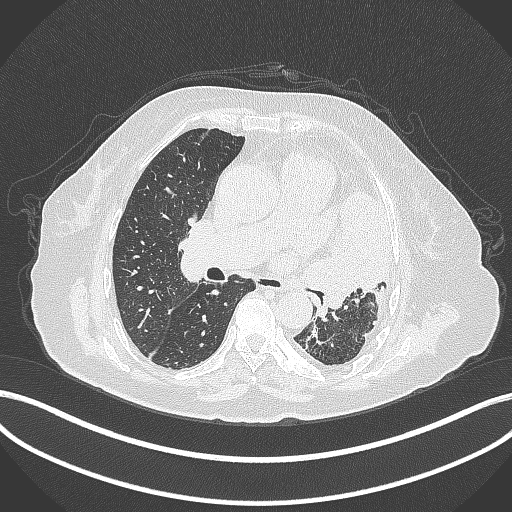
Chest CT, one axial slice. Slice 204 of 399 in the series (ordered by position). Lung window (W 1500 / L -600 HU). 1 mm slice thickness. 512 × 512 image matrix, field of view 400 × 400 mm. Female patient, age 75 years. Case-level facts recorded for this patient, not image findings: clinical TNM (as recorded): T3 N3 M1.
Annotated regions visible in this slice (rectangle marked by the reading radiologist):
- lung tumour (recorded histology: adenocarcinoma): box from (x=296, y=190) to (x=390, y=311) px